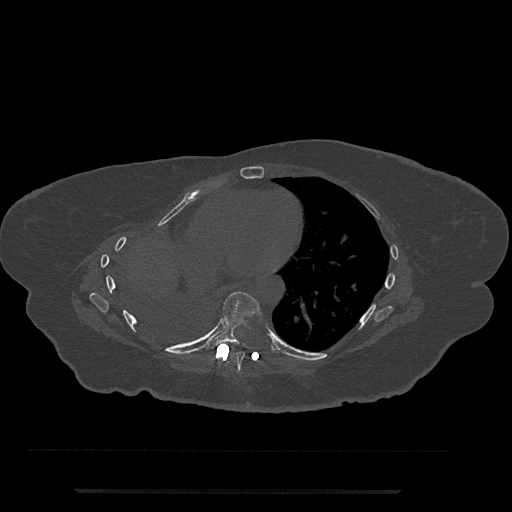
CT including the spine, one axial slice. Slice 408 of 797 in the series (ordered by position). Reconstruction kernel Br40s/3. 120 kVp. Bone window (W 1800 / L 400 HU). 0.5 mm slice thickness. 512 × 512 image matrix, field of view 440 × 440 mm. Patient: female, 51 years. Case-level facts recorded for this patient, not image findings: primary cancer: neuro.
Outlined on this slice (semi-automatically segmented with operator editing):
- T7 vertebra: box from (x=230, y=351) to (x=245, y=374) px
- T8 vertebra: (x=206, y=292)–(x=262, y=350)